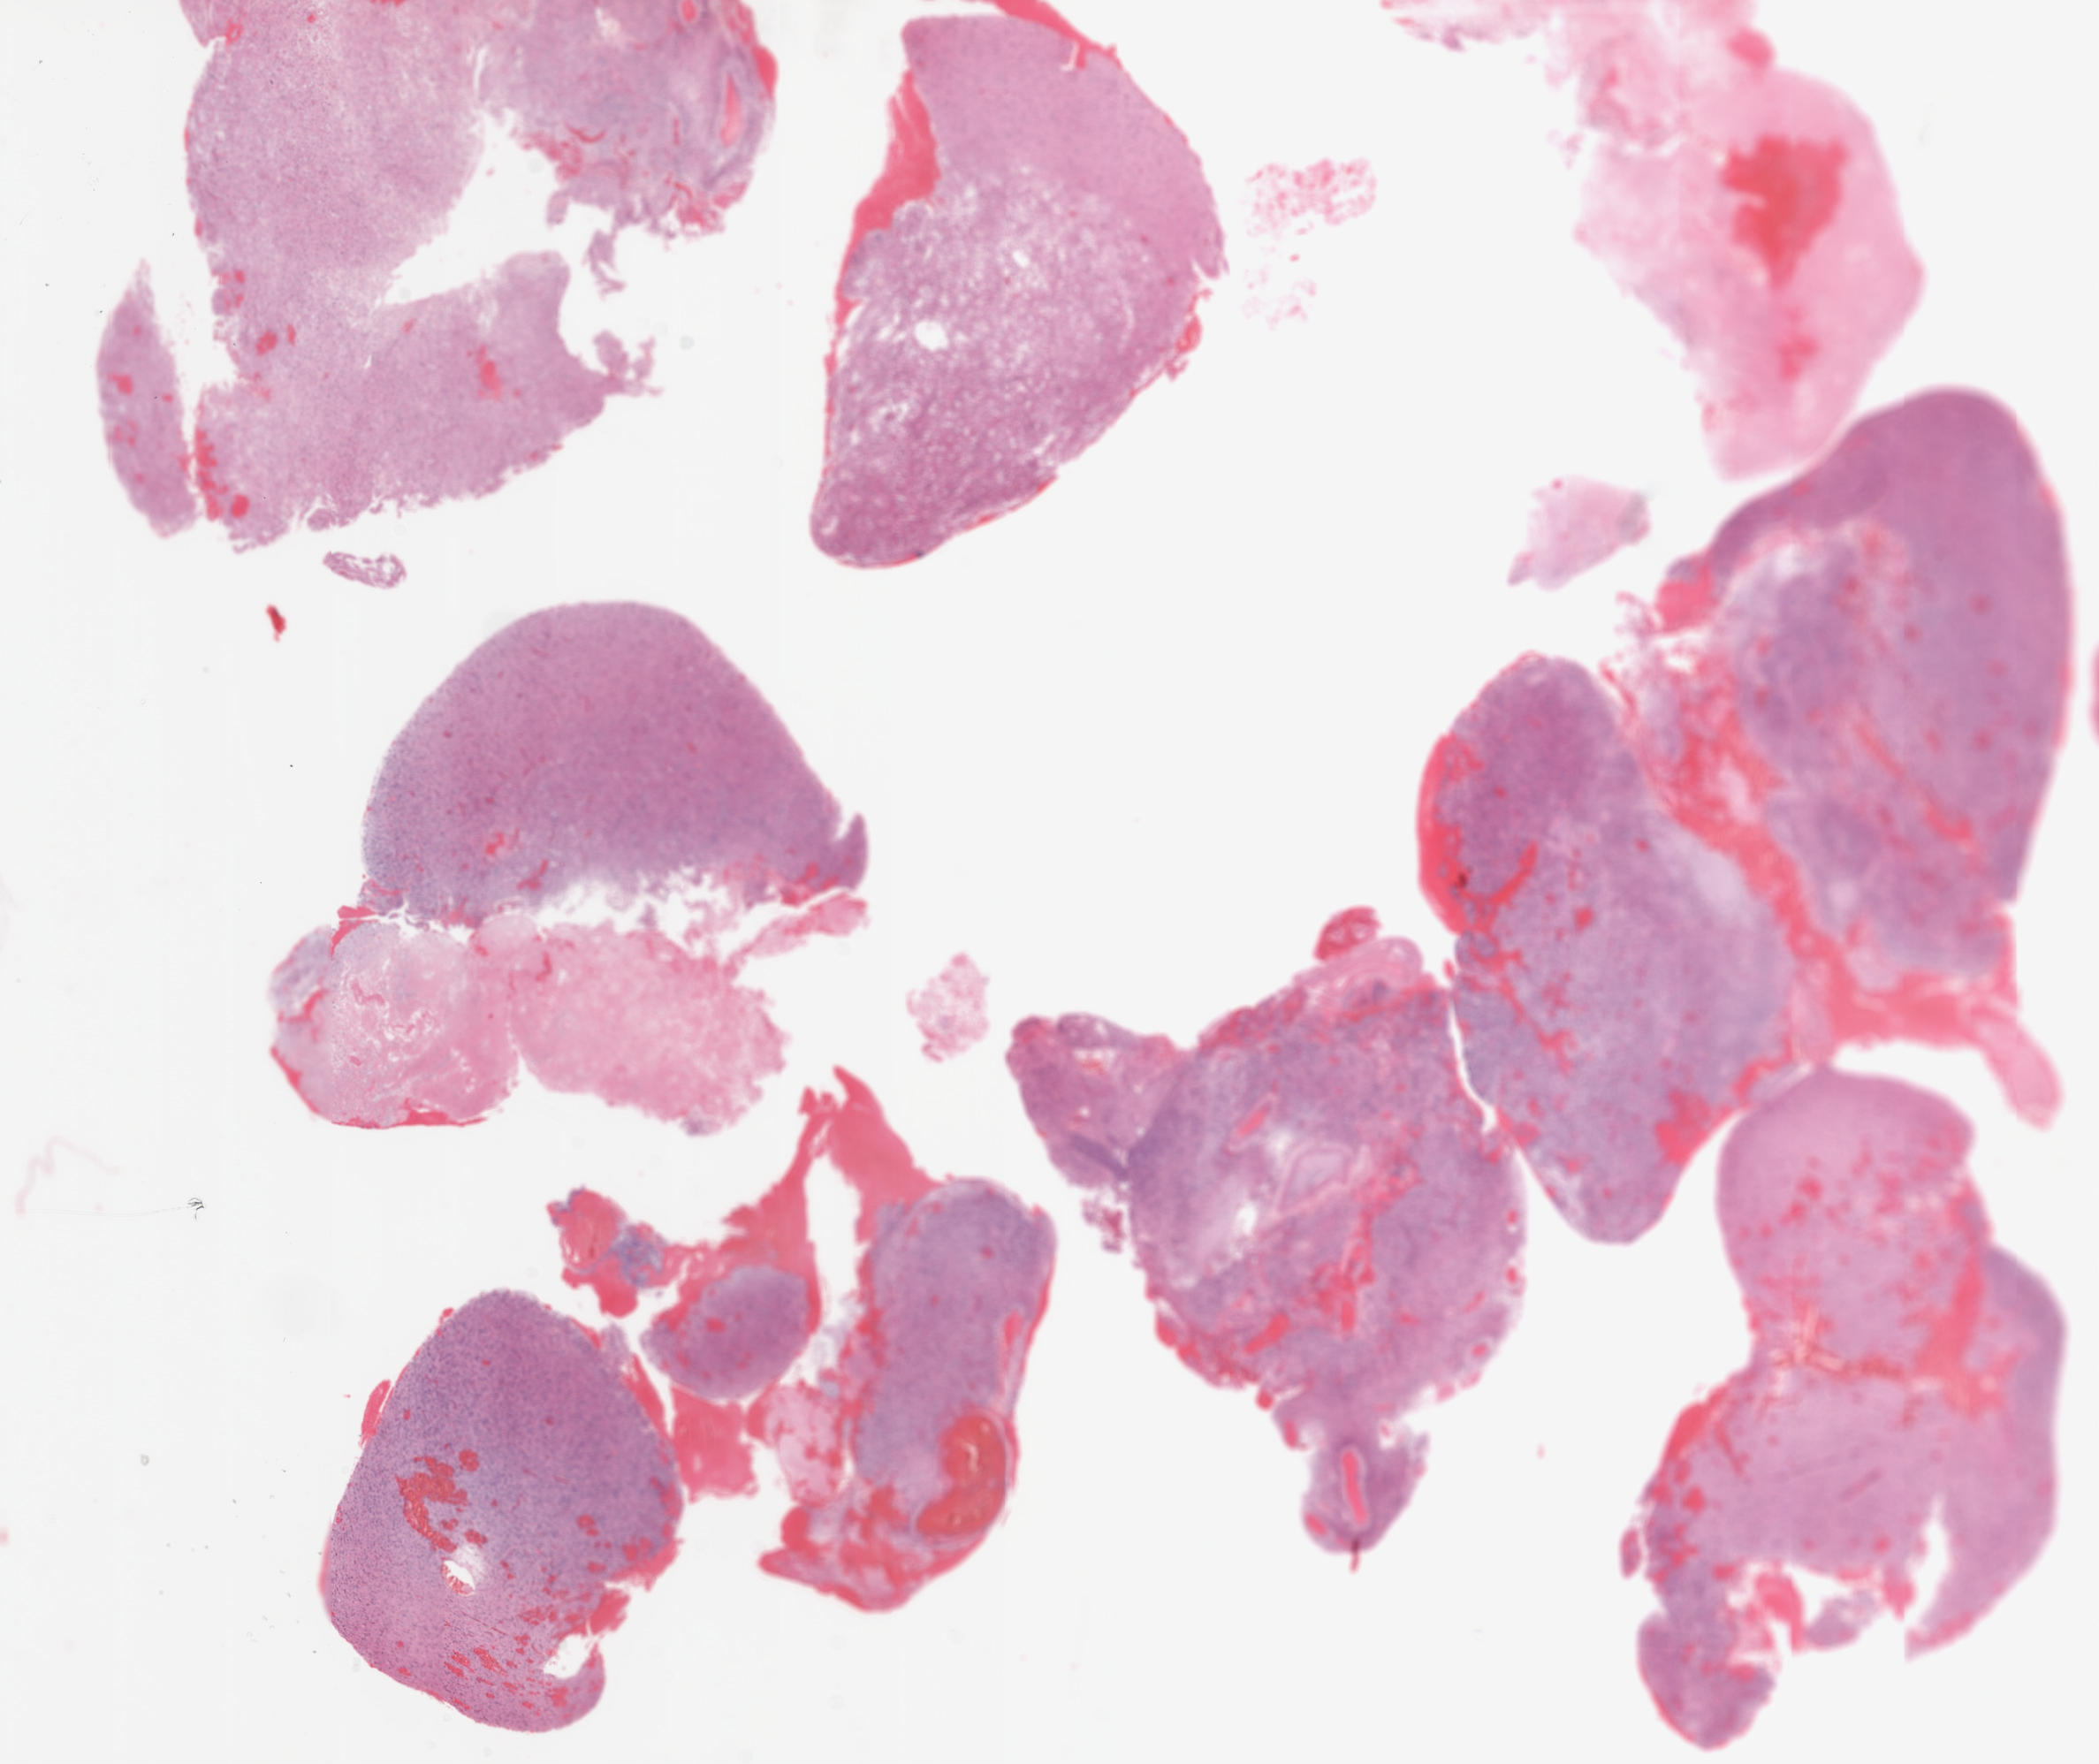
Whole-slide histology image, Hematoxylin and eosin (H&E) stained — low-resolution overview of the scanned area, about 19.1 x 16.0 mm (from a 20x scan). FFPE section. Sample: primary tumour, brain. Male, age 54 years at initial diagnosis.
* diagnosis: Glioblastoma